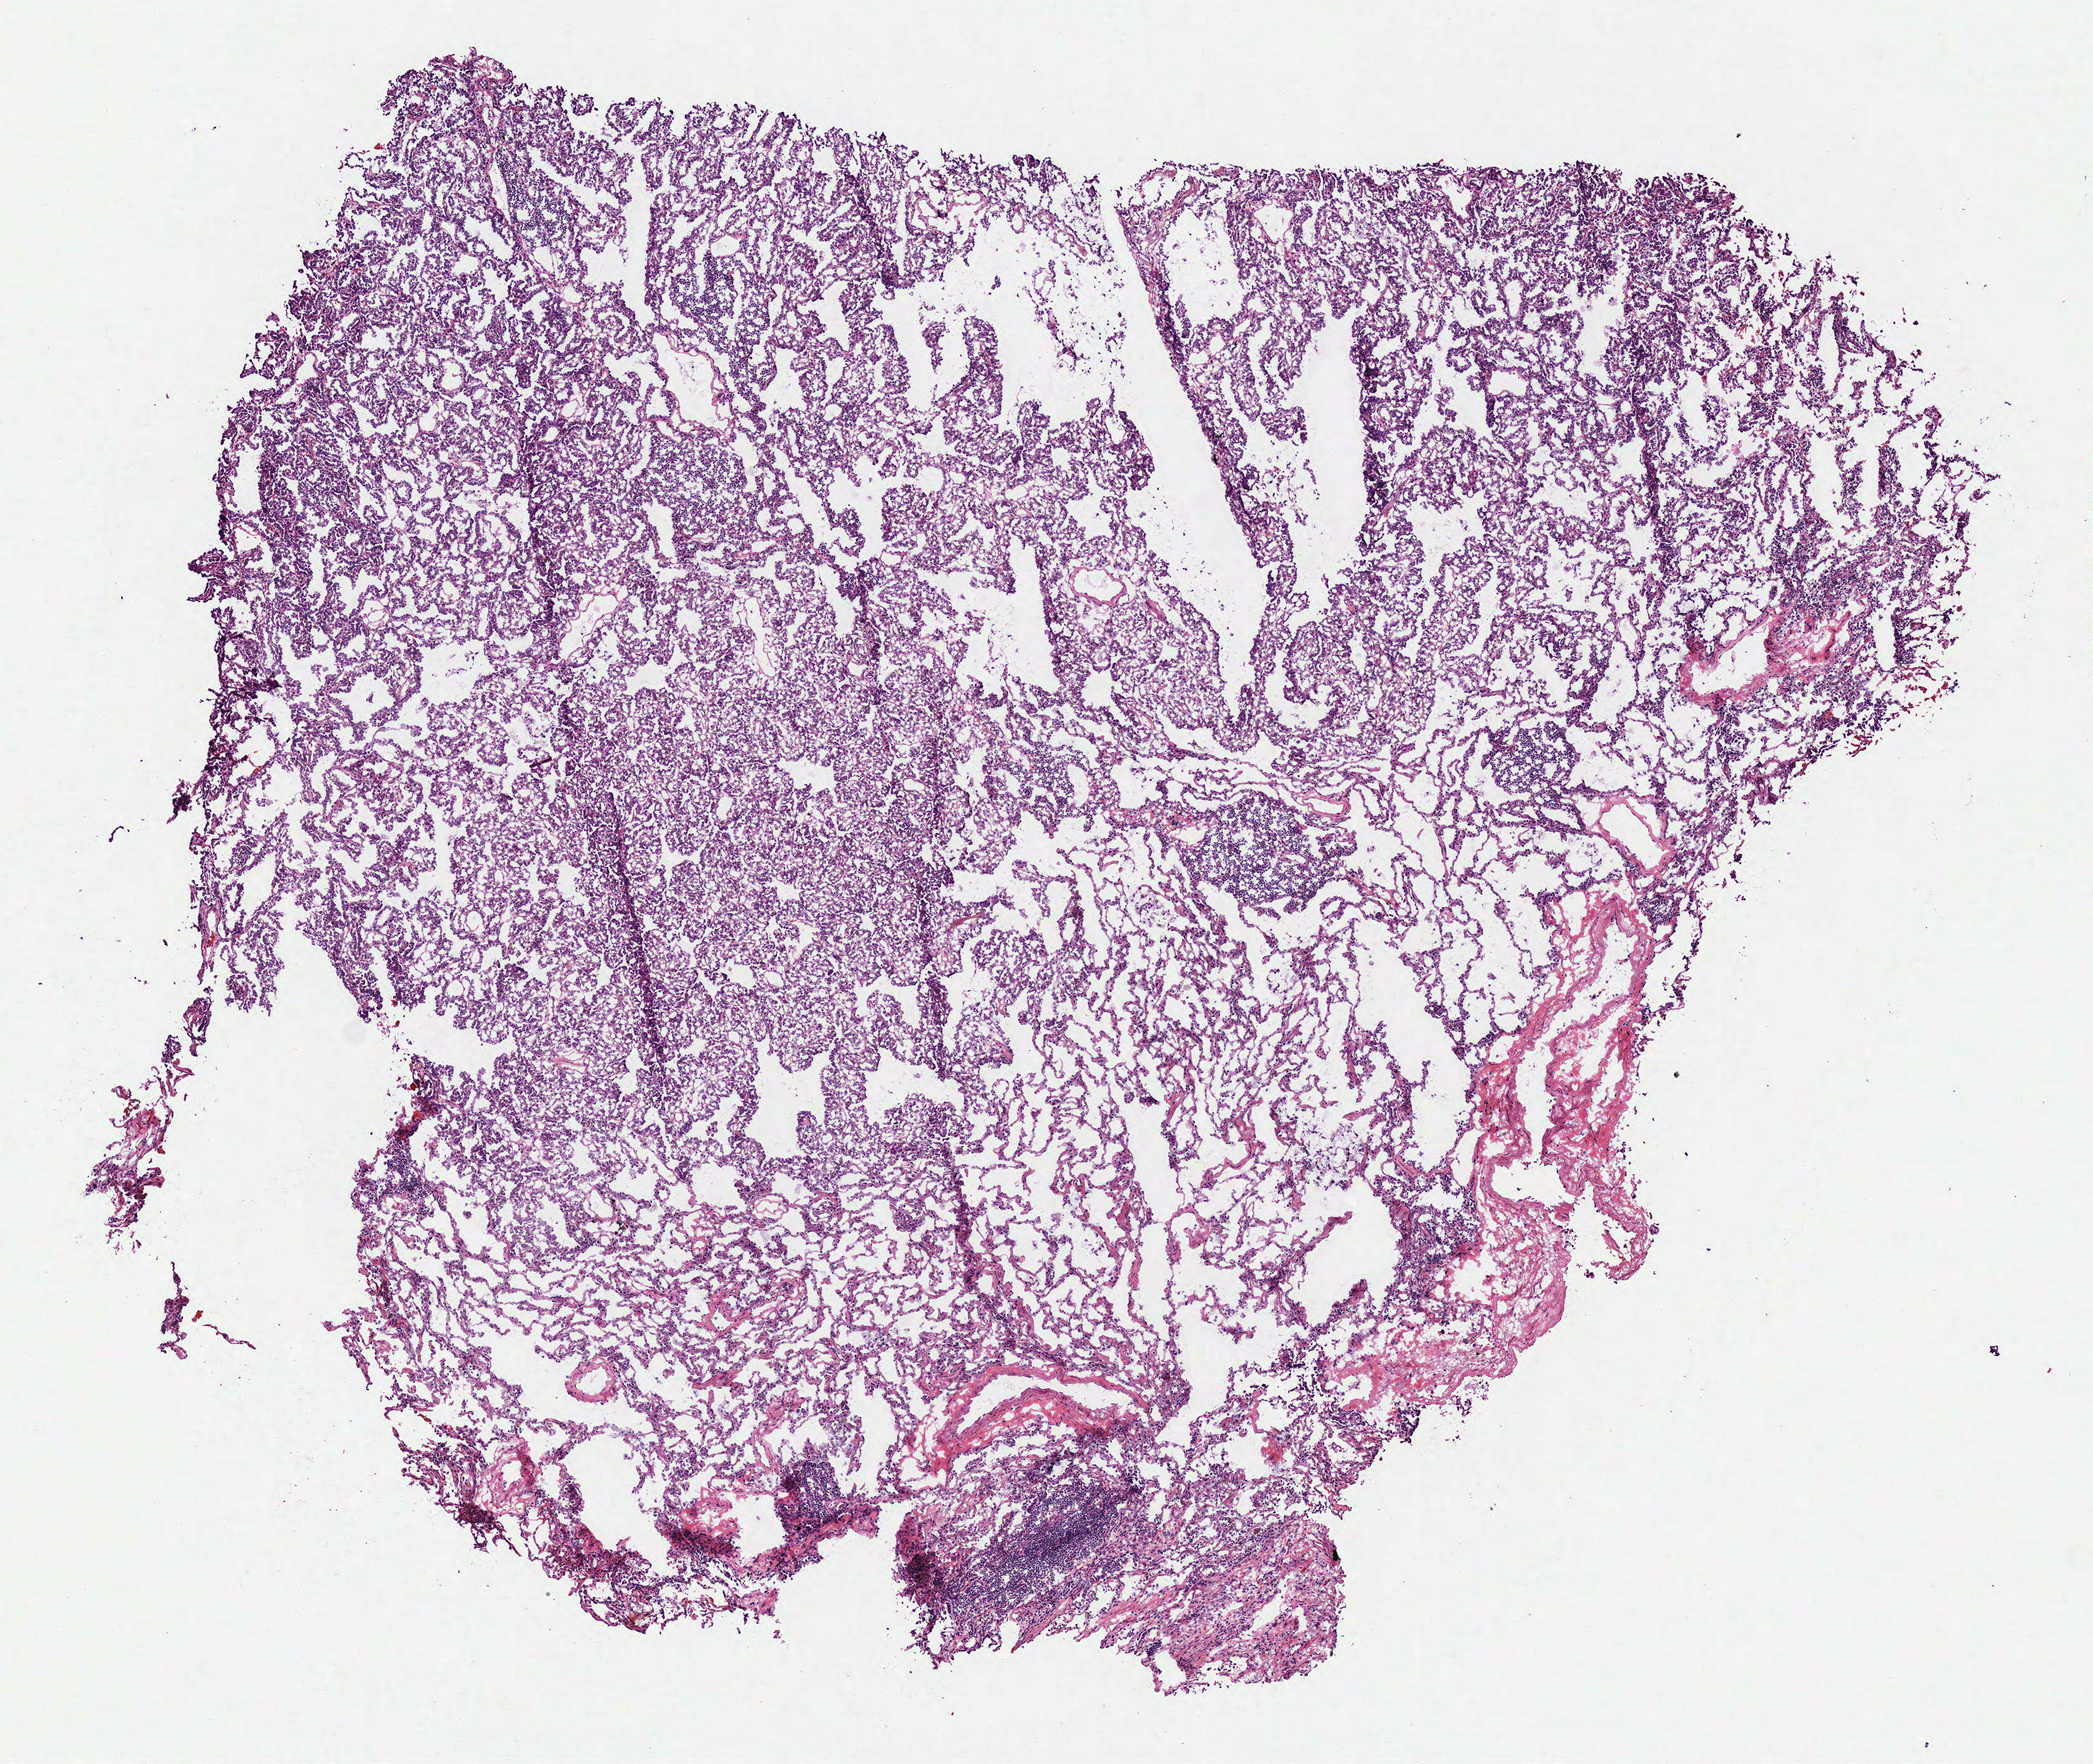
Whole-slide histology image, Hematoxylin and eosin (H&E) stained — low-resolution overview of the scanned area, about 6.6 x 5.5 mm (acquisition: 40x scan). Frozen section. Primary tumour sample from the lung. Male patient; age at initial diagnosis 75 years. Slide review estimates, as recorded: tumour cells 65%, tumour nuclei 60%, normal cells 30%, stromal cells 5%, necrosis 0%.
Histologic diagnosis: Adenocarcinoma with mixed subtypes (upper lobe, lung). AJCC pathologic stage: IA (6th edition). TNM: T1 N0 M0.